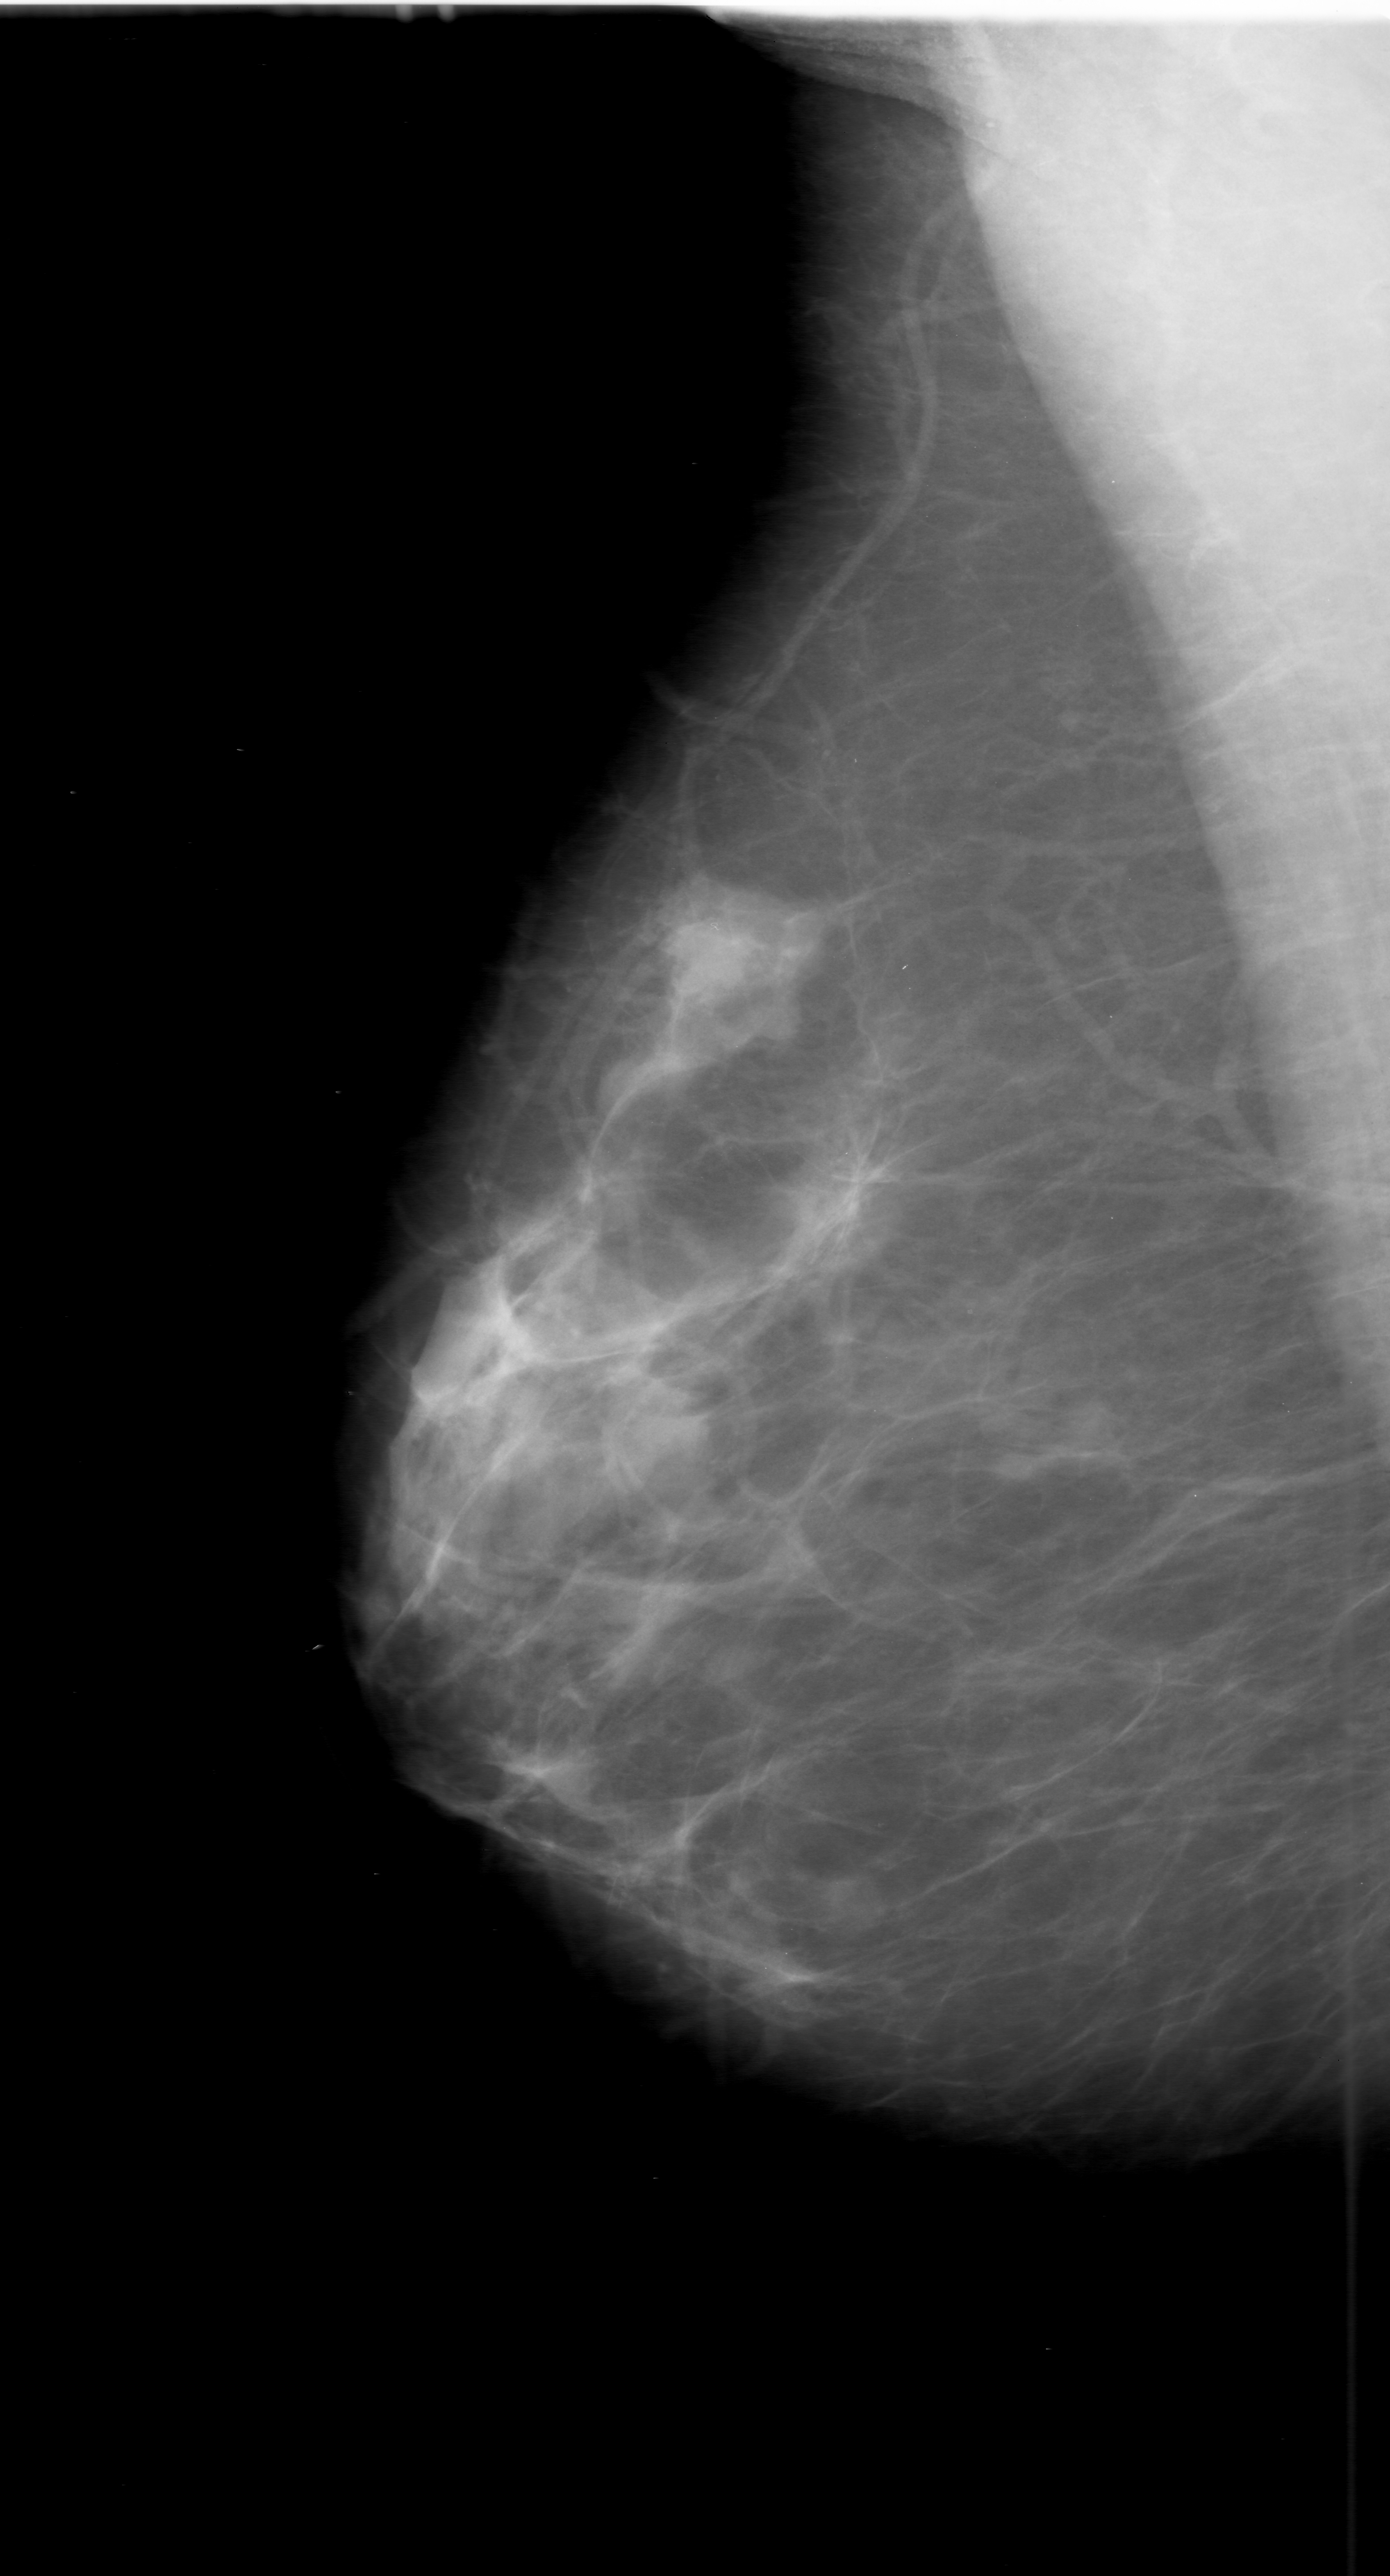
Scanned film-screen mammogram, right breast, MLO view, breast composition: scattered fibroglandular densities (BI-RADS density category 2 of 4).
Abnormality record for this image: mass, shape irregular, margins ill defined; BI-RADS assessment category 3; subtlety rating 5 on a 1 (subtle) to 5 (obvious) scale; pathology (as recorded): malignant.